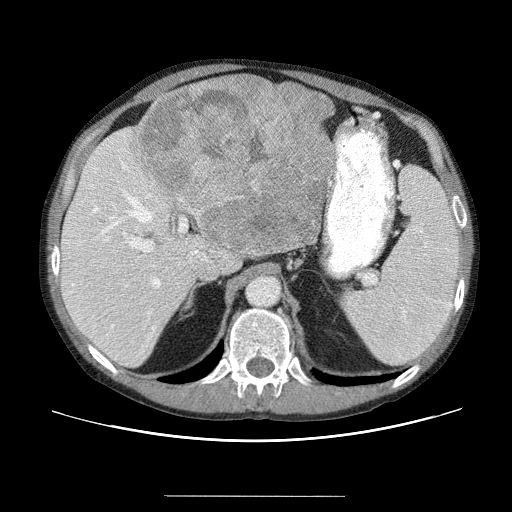
Contrast-enhanced abdominal CT (liver protocol), one axial slice; position 33 of 69 along the scan axis; reconstruction kernel STANDARD; soft-tissue window (W 400 / L 40 HU); 2.5 mm slice thickness; 512 × 512 image matrix, field of view 380 × 380 mm. From the clinical record (not read from this slice): diagnosis: hepatocellular carcinoma (patient treated with transarterial chemoembolisation; whether this scan precedes or follows treatment is not stated here); TNM stage (as recorded): Stage-IVB; Child-Pugh class: B; tumour differentiation: poorly differentiated.
Annotated regions visible in this slice (semi-automatic segmentation, software-assisted and operator-edited):
- abdominal aorta: bounding box [x1, y1, x2, y2] px = [246, 276, 279, 306]
- liver parenchyma outside the tumour (the mass and vessels are separate outlines, so this box may not span the whole liver): [60, 126, 334, 366]
- mass: [133, 75, 335, 256]
- liver vessels: [71, 152, 223, 341]